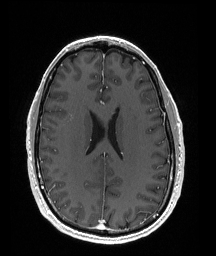
Brain MRI from a brain-tumour surgery series, one axial slice; position 72 of 176 along the scan axis; T1-weighted post-contrast; 1 mm slice thickness; 216 × 256 image matrix, field of view 211 × 250 mm. Case-level facts recorded for this patient, not image findings: histopathology: Oligodendroglioma; WHO grade: 2; IDH mutation: yes; tumour location: Right Parietal.
Annotated regions visible in this slice (outlined manually by an expert reader):
- tumour: bounding box <92,182,99,188> (left, top, right, bottom; pixels)